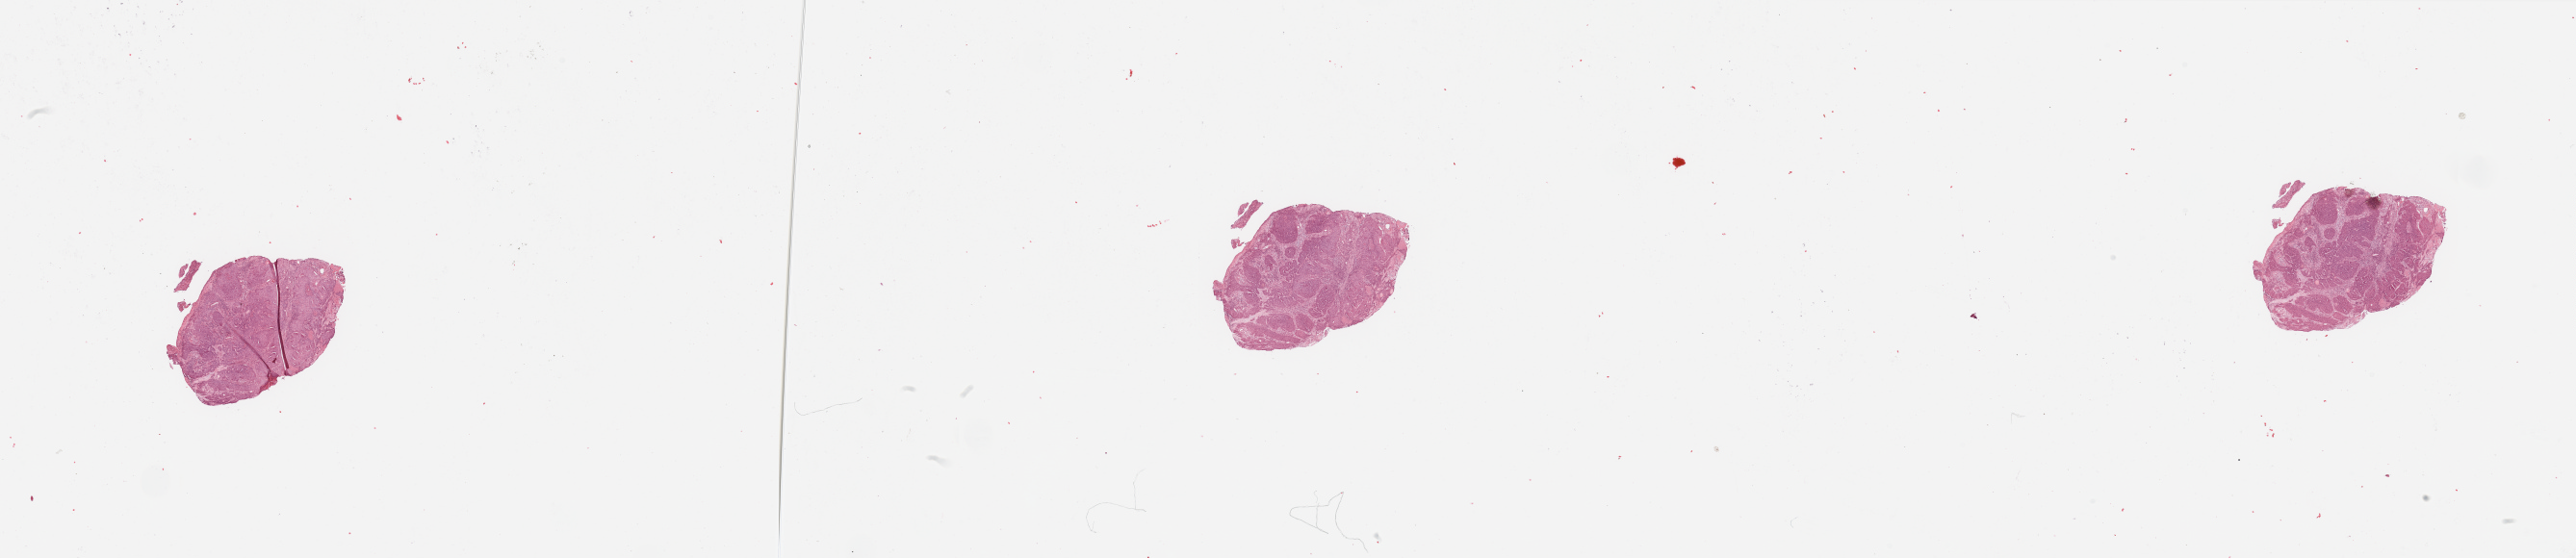
H&E whole-slide image, whole scanned area (about 42.3 x 9.2 mm, slide scanned at 20x) shown as a low-resolution overview. Tumour tissue sample, sampled site: larynx. 62-year-old male patient. Histologic grade: G3 (poorly differentiated). Pathologist review of this section (percent, as recorded): tumour nuclei 85%, necrosis 2%.
AJCC pathologic stage: IVA. Histologic diagnosis: Squamous cell carcinoma, NOS (larynx, NOS).